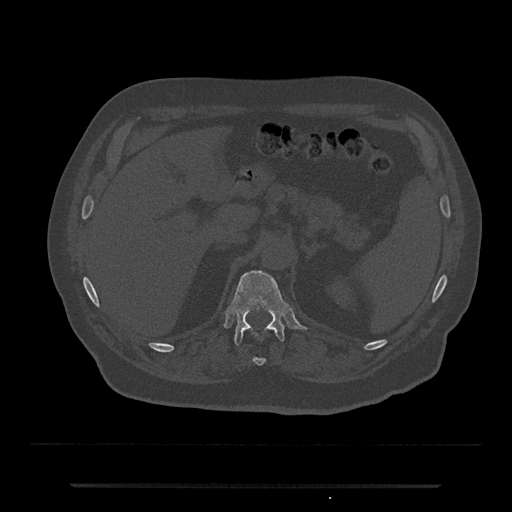
CT including the spine, one axial slice. 120 kVp. Bone window (W 1800 / L 400 HU). 512 × 512 image matrix, field of view 434 × 434 mm. Patient: male, 80 years. From the clinical record (not read from this slice): primary cancer: prostate.
Outlined on this slice (semi-automatic segmentation, software-assisted and operator-edited):
- T11 vertebra: bounding box [x1, y1, x2, y2] px = [253, 357, 265, 366]
- T12 vertebra: [228, 270, 289, 345]